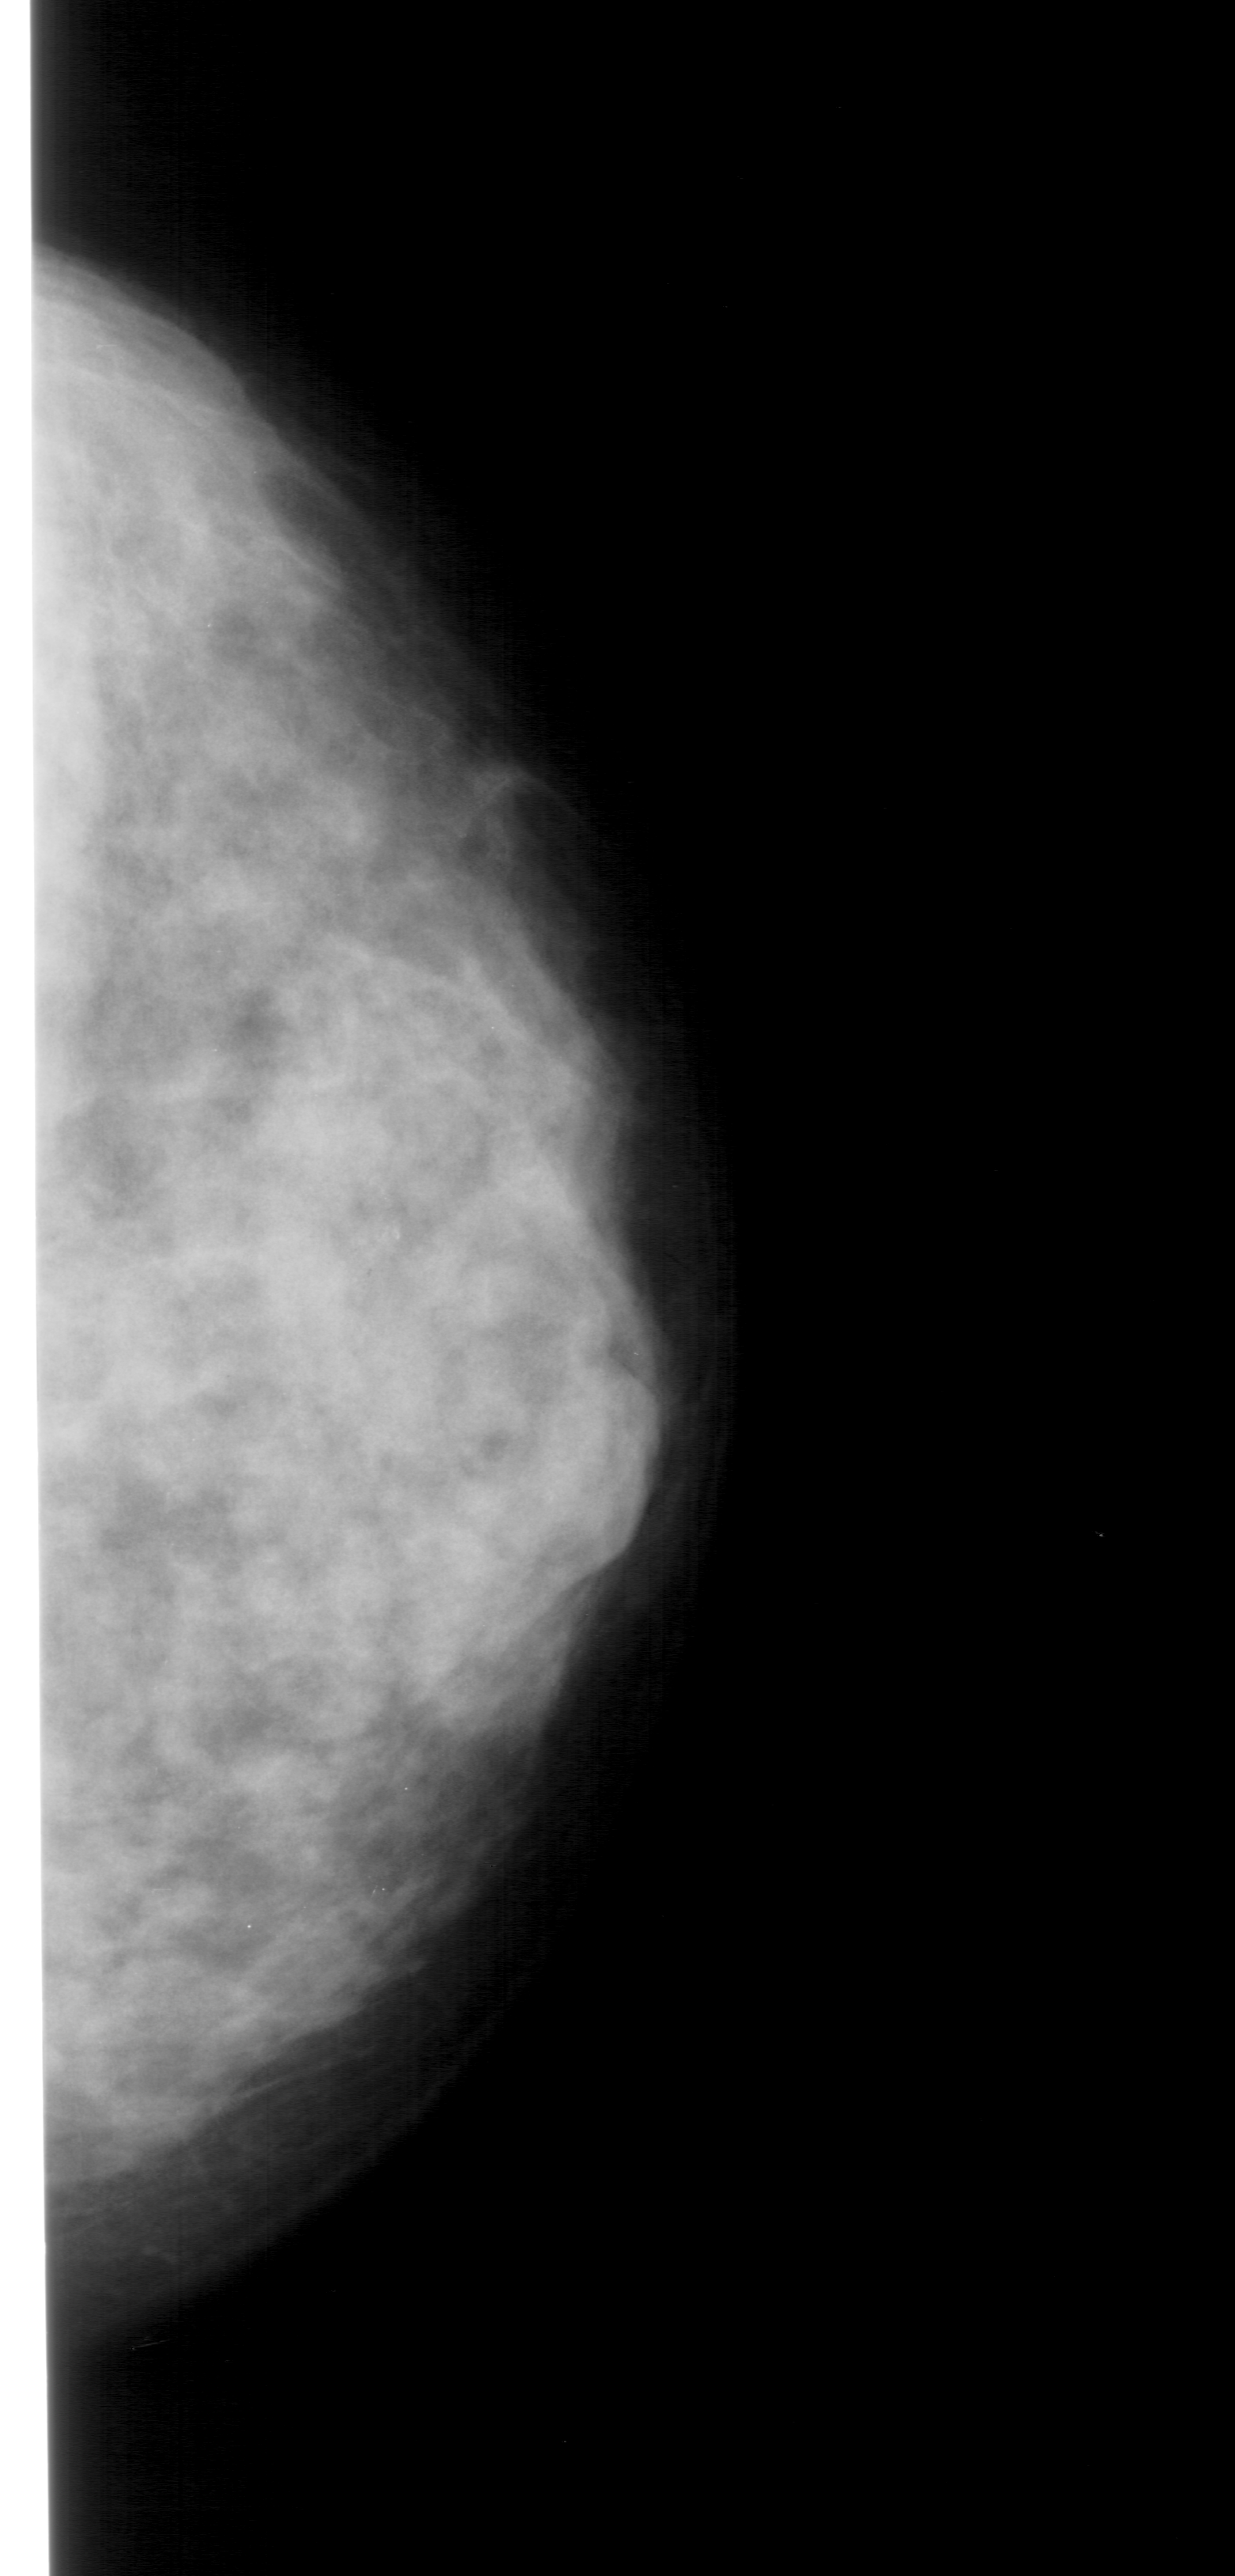
Mammogram (digitized film). Right breast. CC view. 1235 × 2576 image matrix.
Marked abnormalities (boxes around the expert regions of interest):
- calcifications, morphology pleomorphic, distribution clustered; BI-RADS assessment category 4; pathology (as recorded): benign: bounding box [x1, y1, x2, y2] px = [347, 1173, 444, 1285]